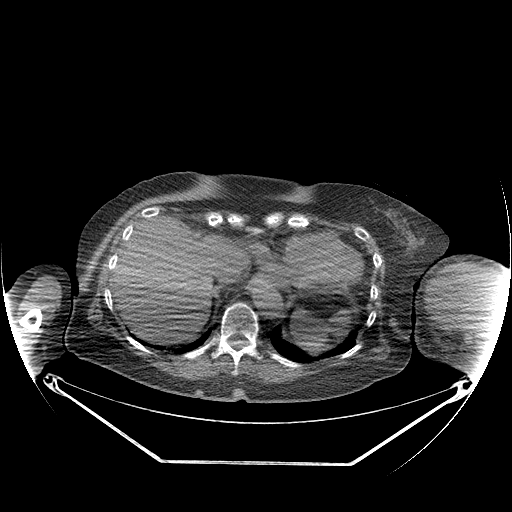
CT of an extremity soft-tissue mass (from a PET/CT study), one axial slice; slice 143 of 267 in the series (ordered by position); soft-tissue window (W 400 / L 40 HU); 3.75 mm slice thickness; 512 × 512 image matrix, field of view 500 × 500 mm. Female patient. From the clinical record (not read from this slice): histological type: pleiomorphic leiomyosarcoma; grade: high; site of the primary tumour: left biceps.
Outlined on this slice (expert contour drawn on MRI and transferred to this co-registered scan by the dataset authors):
- gross tumour volume including surrounding oedema: bounding box [x1, y1, x2, y2] px = [436, 267, 501, 321]
- gross tumour volume (mass): [436, 267, 499, 312]